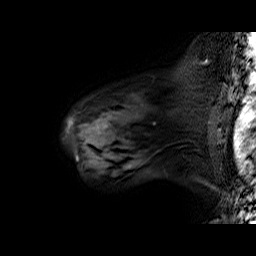
Breast MRI (dynamic contrast-enhanced), one sagittal slice. Position 47 of 60 along the scan axis. Dynamic contrast-enhanced series, time point 2 of 6 at this slice position (early post-contrast). 1.5 T. TE 6.4 ms, TR 32.9 ms. 256 × 256 image matrix, field of view 200 × 200 mm. Female patient. Case-level facts recorded for this patient, not image findings: setting: breast cancer imaged before/during neoadjuvant chemotherapy; receptor status: HER2-positive.
Annotated regions visible in this slice (semi-automatic segmentation, software-assisted and operator-edited):
- analysis volume of interest (the breast-tissue region the enhancement analysis was run in; not a lesion): bounding box [x1, y1, x2, y2] px = [64, 78, 196, 160]
- tumour enhancement mask (voxels above the 100 % enhancement threshold inside the analysis volume of interest): [66, 118, 79, 160]